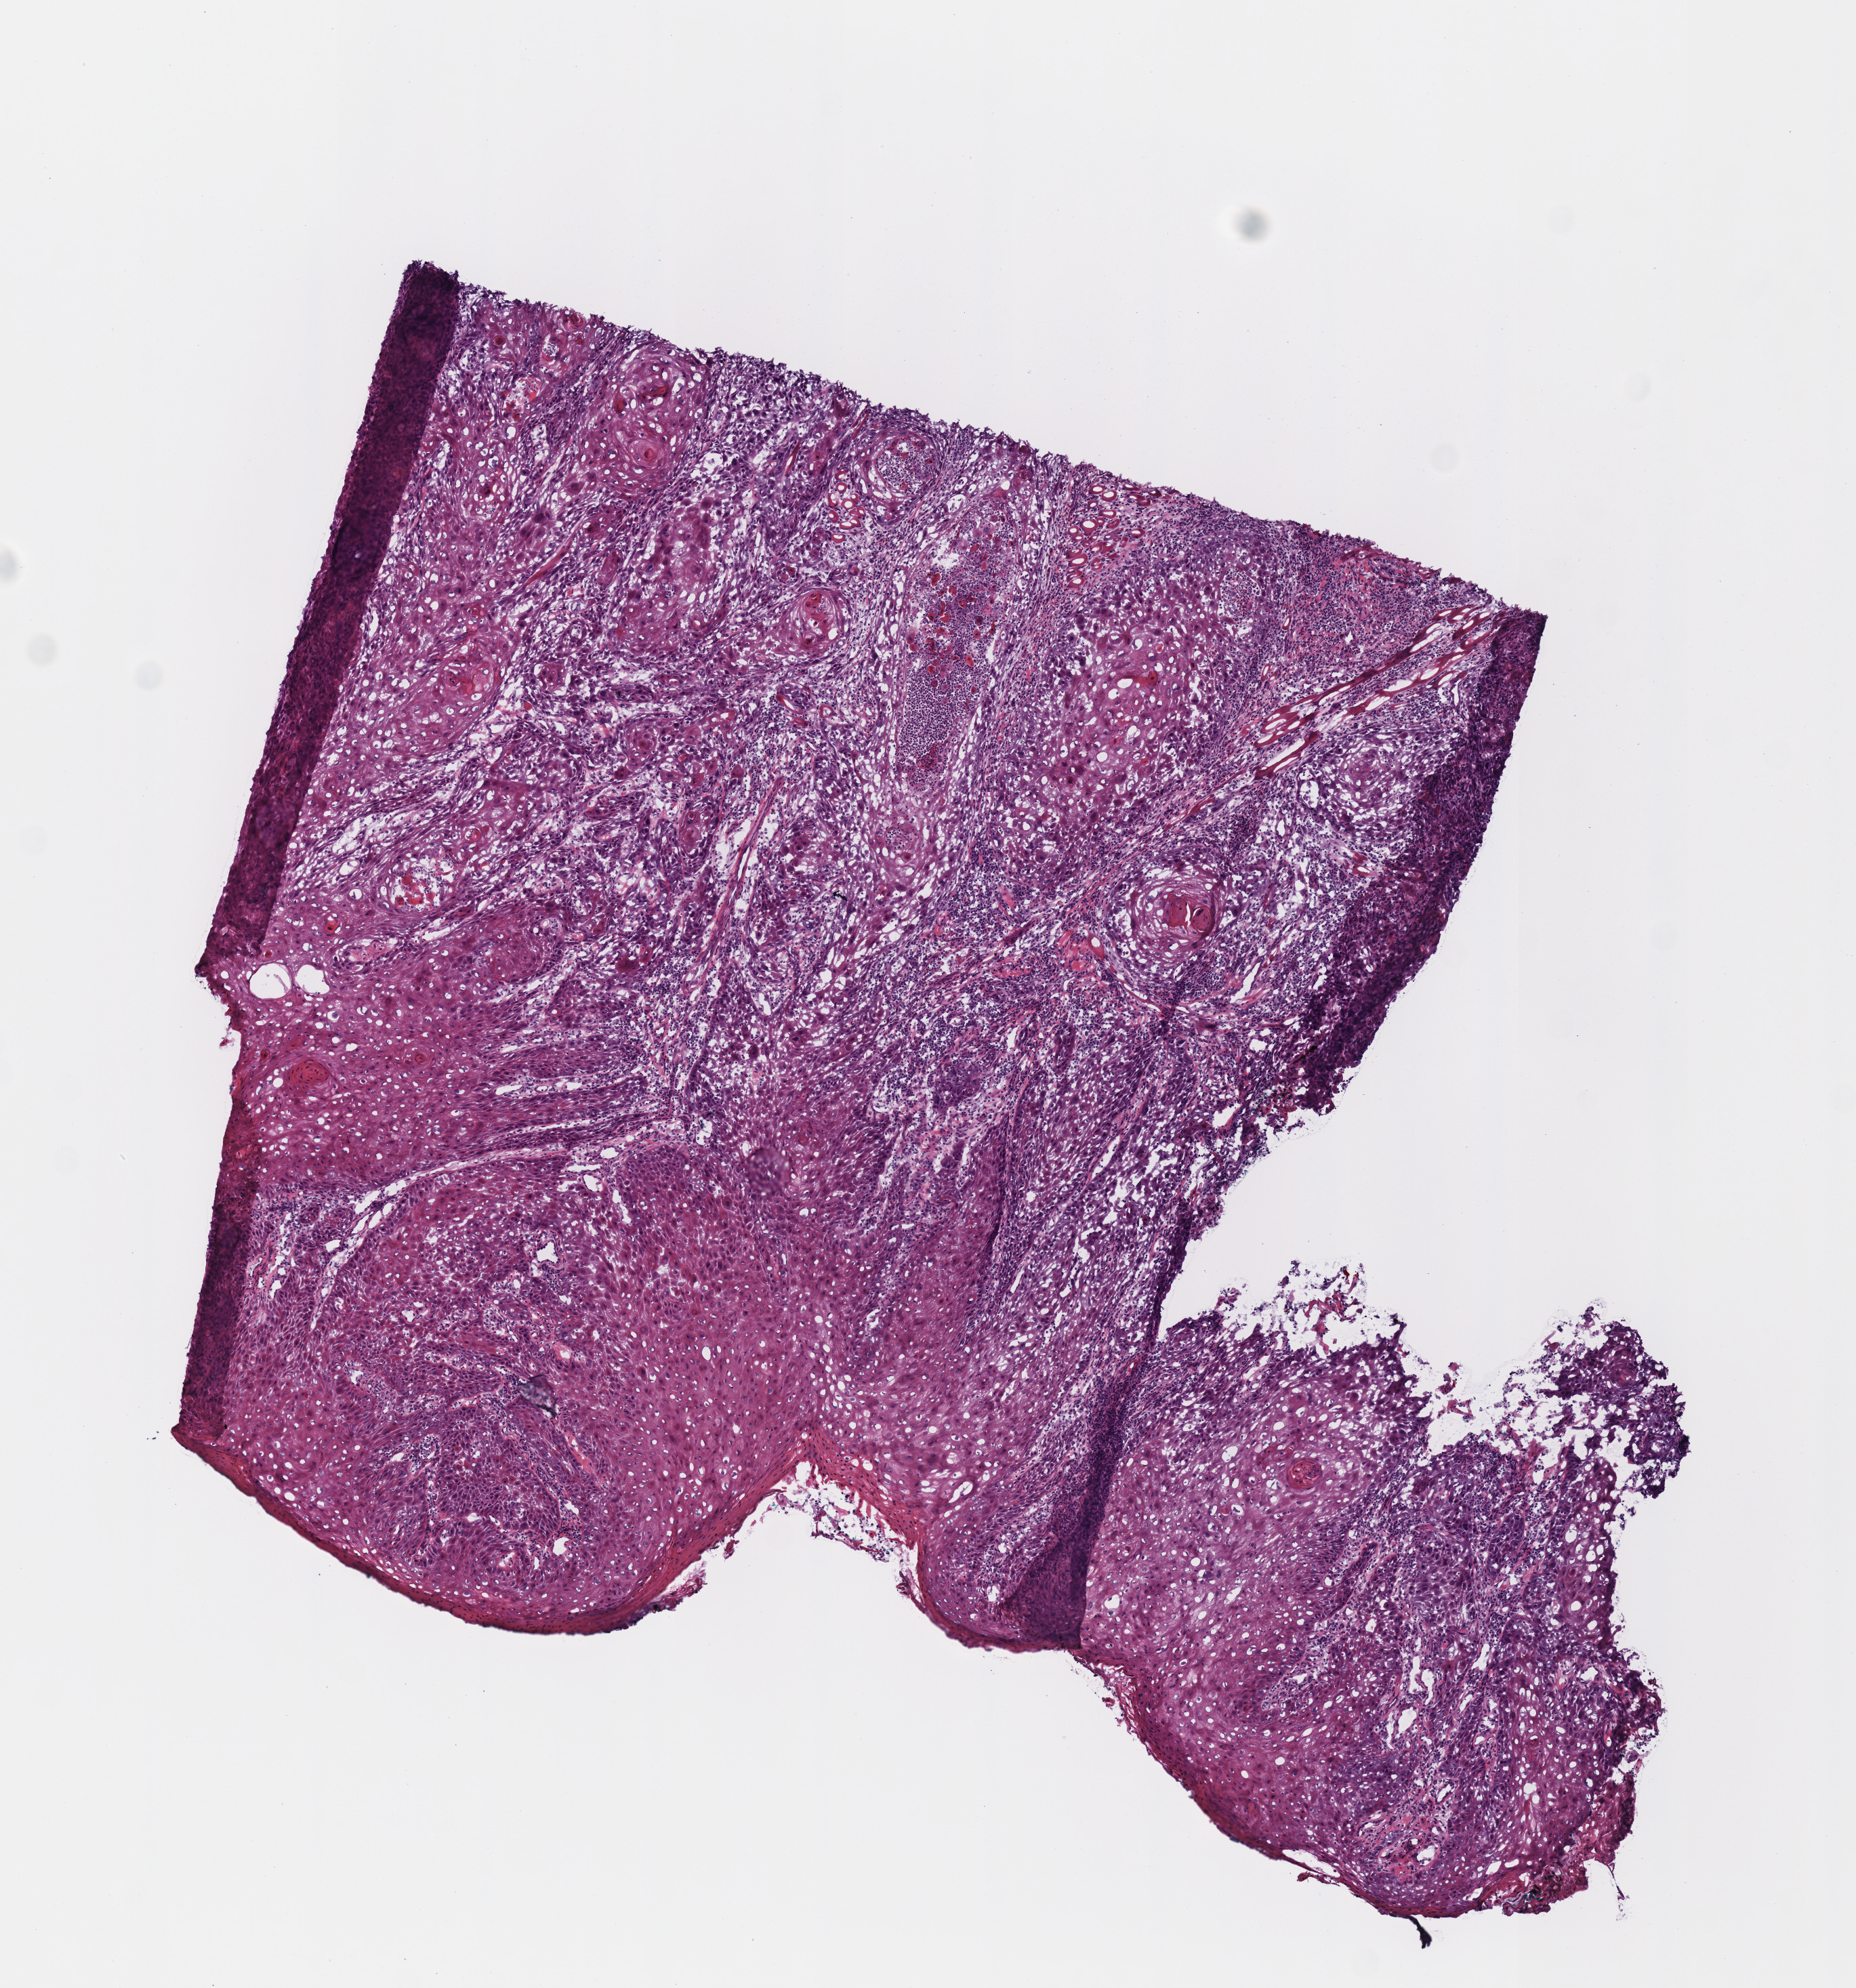
Whole-slide histology image, H&E, low-resolution overview of the scanned area, about 5.4 x 5.8 mm (slide scanned at 40x); frozen section from the top of the tissue portion; sample: primary tumour, head and neck. Patient: female, age at initial diagnosis 51 years. Histologic grade: G2 (moderately differentiated). Composition of this section per pathologist review: tumour cells 80%, tumour nuclei 65%, normal cells 0%, stromal cells 20%, necrosis 0%.
* laterality: left
* AJCC pathologic stage: I (7th edition)
* diagnosis: Squamous cell carcinoma, NOS (tongue, NOS)